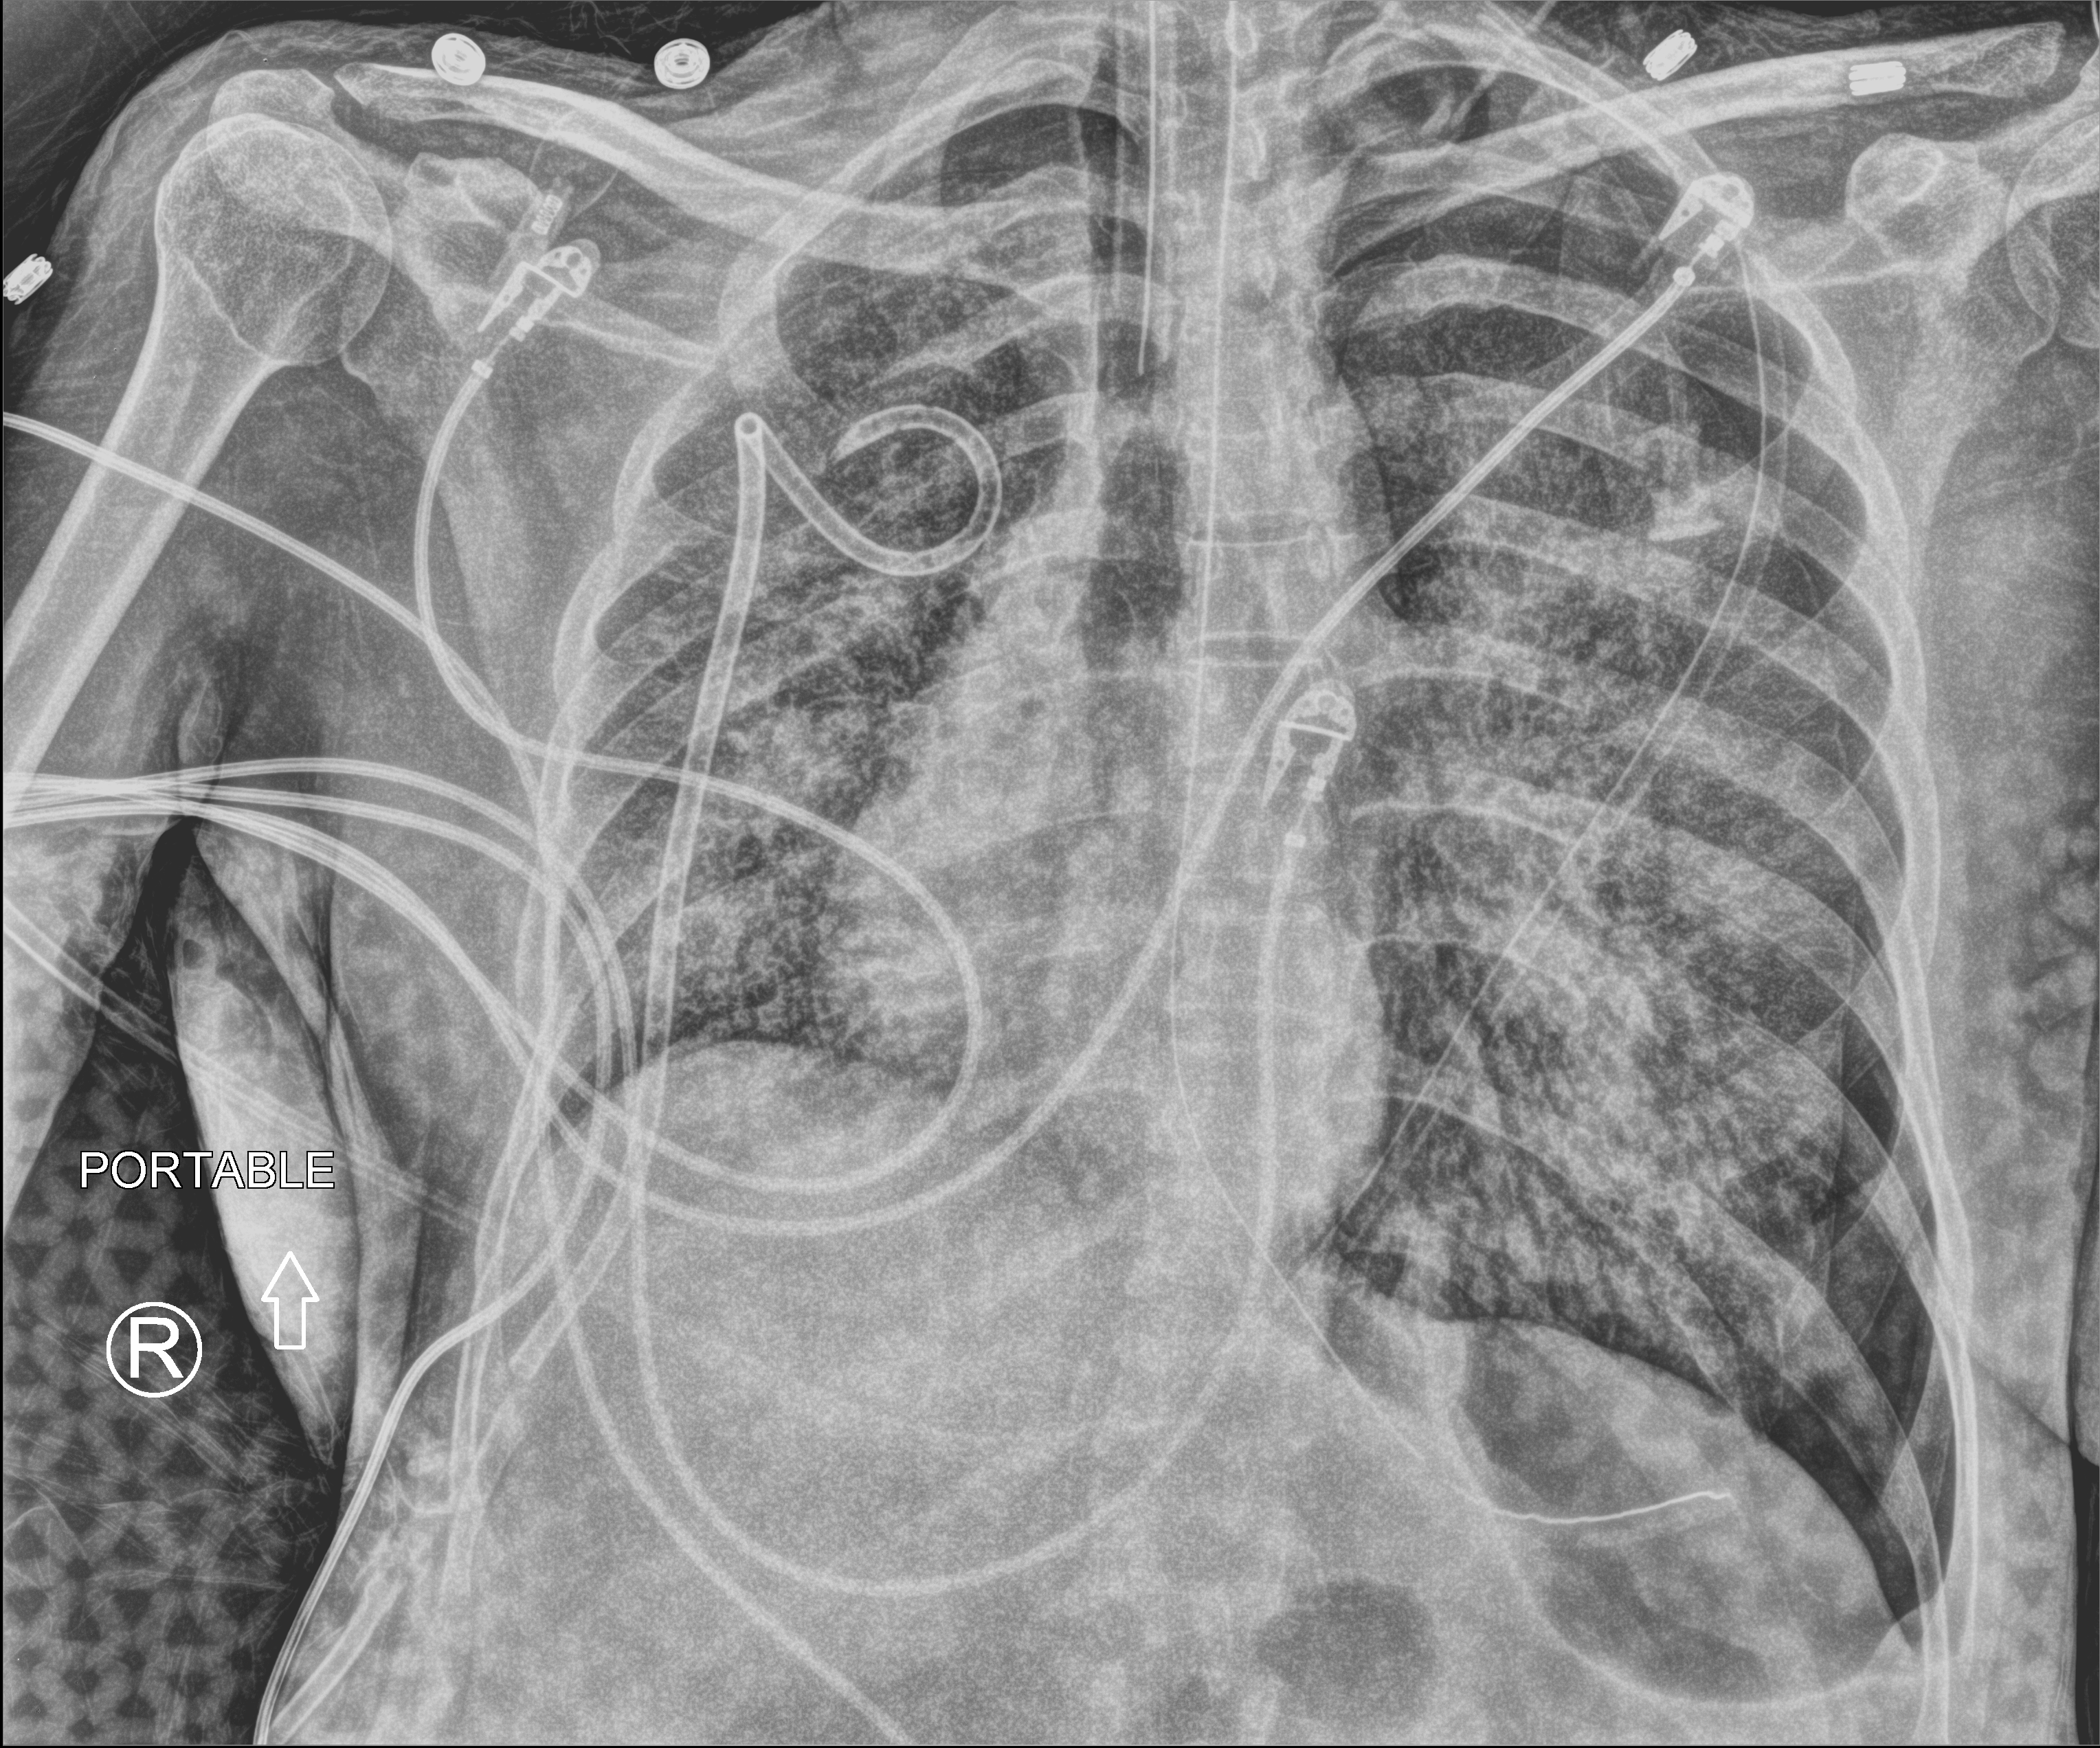
Bedside chest radiograph (computed radiography). Adult patient hospitalised with COVID-19, age 18–59 years.
From the hospital-stay record, not from the radiograph (when in the stay this image was taken is not recorded): diabetes (admission record): no; mechanically ventilated during this hospital stay: yes.